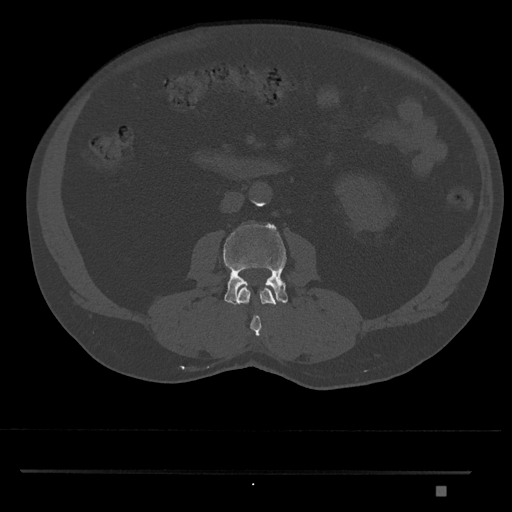
CT including the spine, one axial slice; slice 708 of 1134 in the series (ordered by position); reconstruction kernel Br40s/3; bone window (W 1800 / L 400 HU); 512 × 512 image matrix, field of view 429 × 429 mm. Patient: male, 65 years. Case-level facts recorded for this patient, not image findings: primary cancer: prostate.
Outlined on this slice (semi-automatic segmentation, software-assisted and operator-edited):
- L2 vertebra: bounding box <238,286,276,337> (left, top, right, bottom; pixels)
- L3 vertebra: <223,223,288,305>